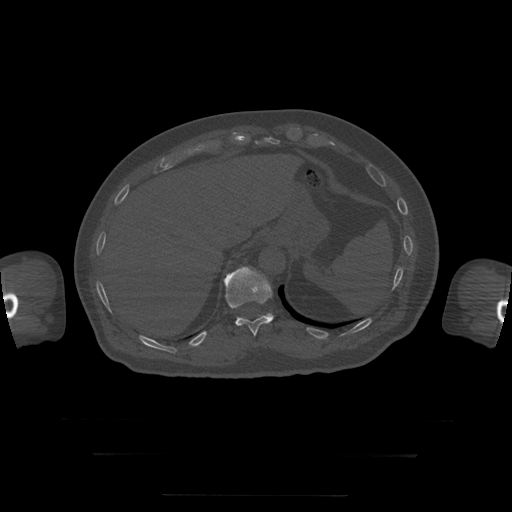
CT including the spine, one axial slice; position 96 of 397 along the scan axis; reconstruction kernel STANDARD; 120 kVp; bone window (W 1800 / L 400 HU); 1.25 mm slice thickness; 512 × 512 image matrix, field of view 510 × 510 mm. Patient age 73 years. From the clinical record (not read from this slice): primary cancer: prostate.
Structures marked on this image (semi-automatic segmentation, software-assisted and operator-edited):
- T11 vertebra: box from (x=224, y=267) to (x=274, y=336) px
- T12 vertebra: (x=237, y=314)–(x=273, y=320)